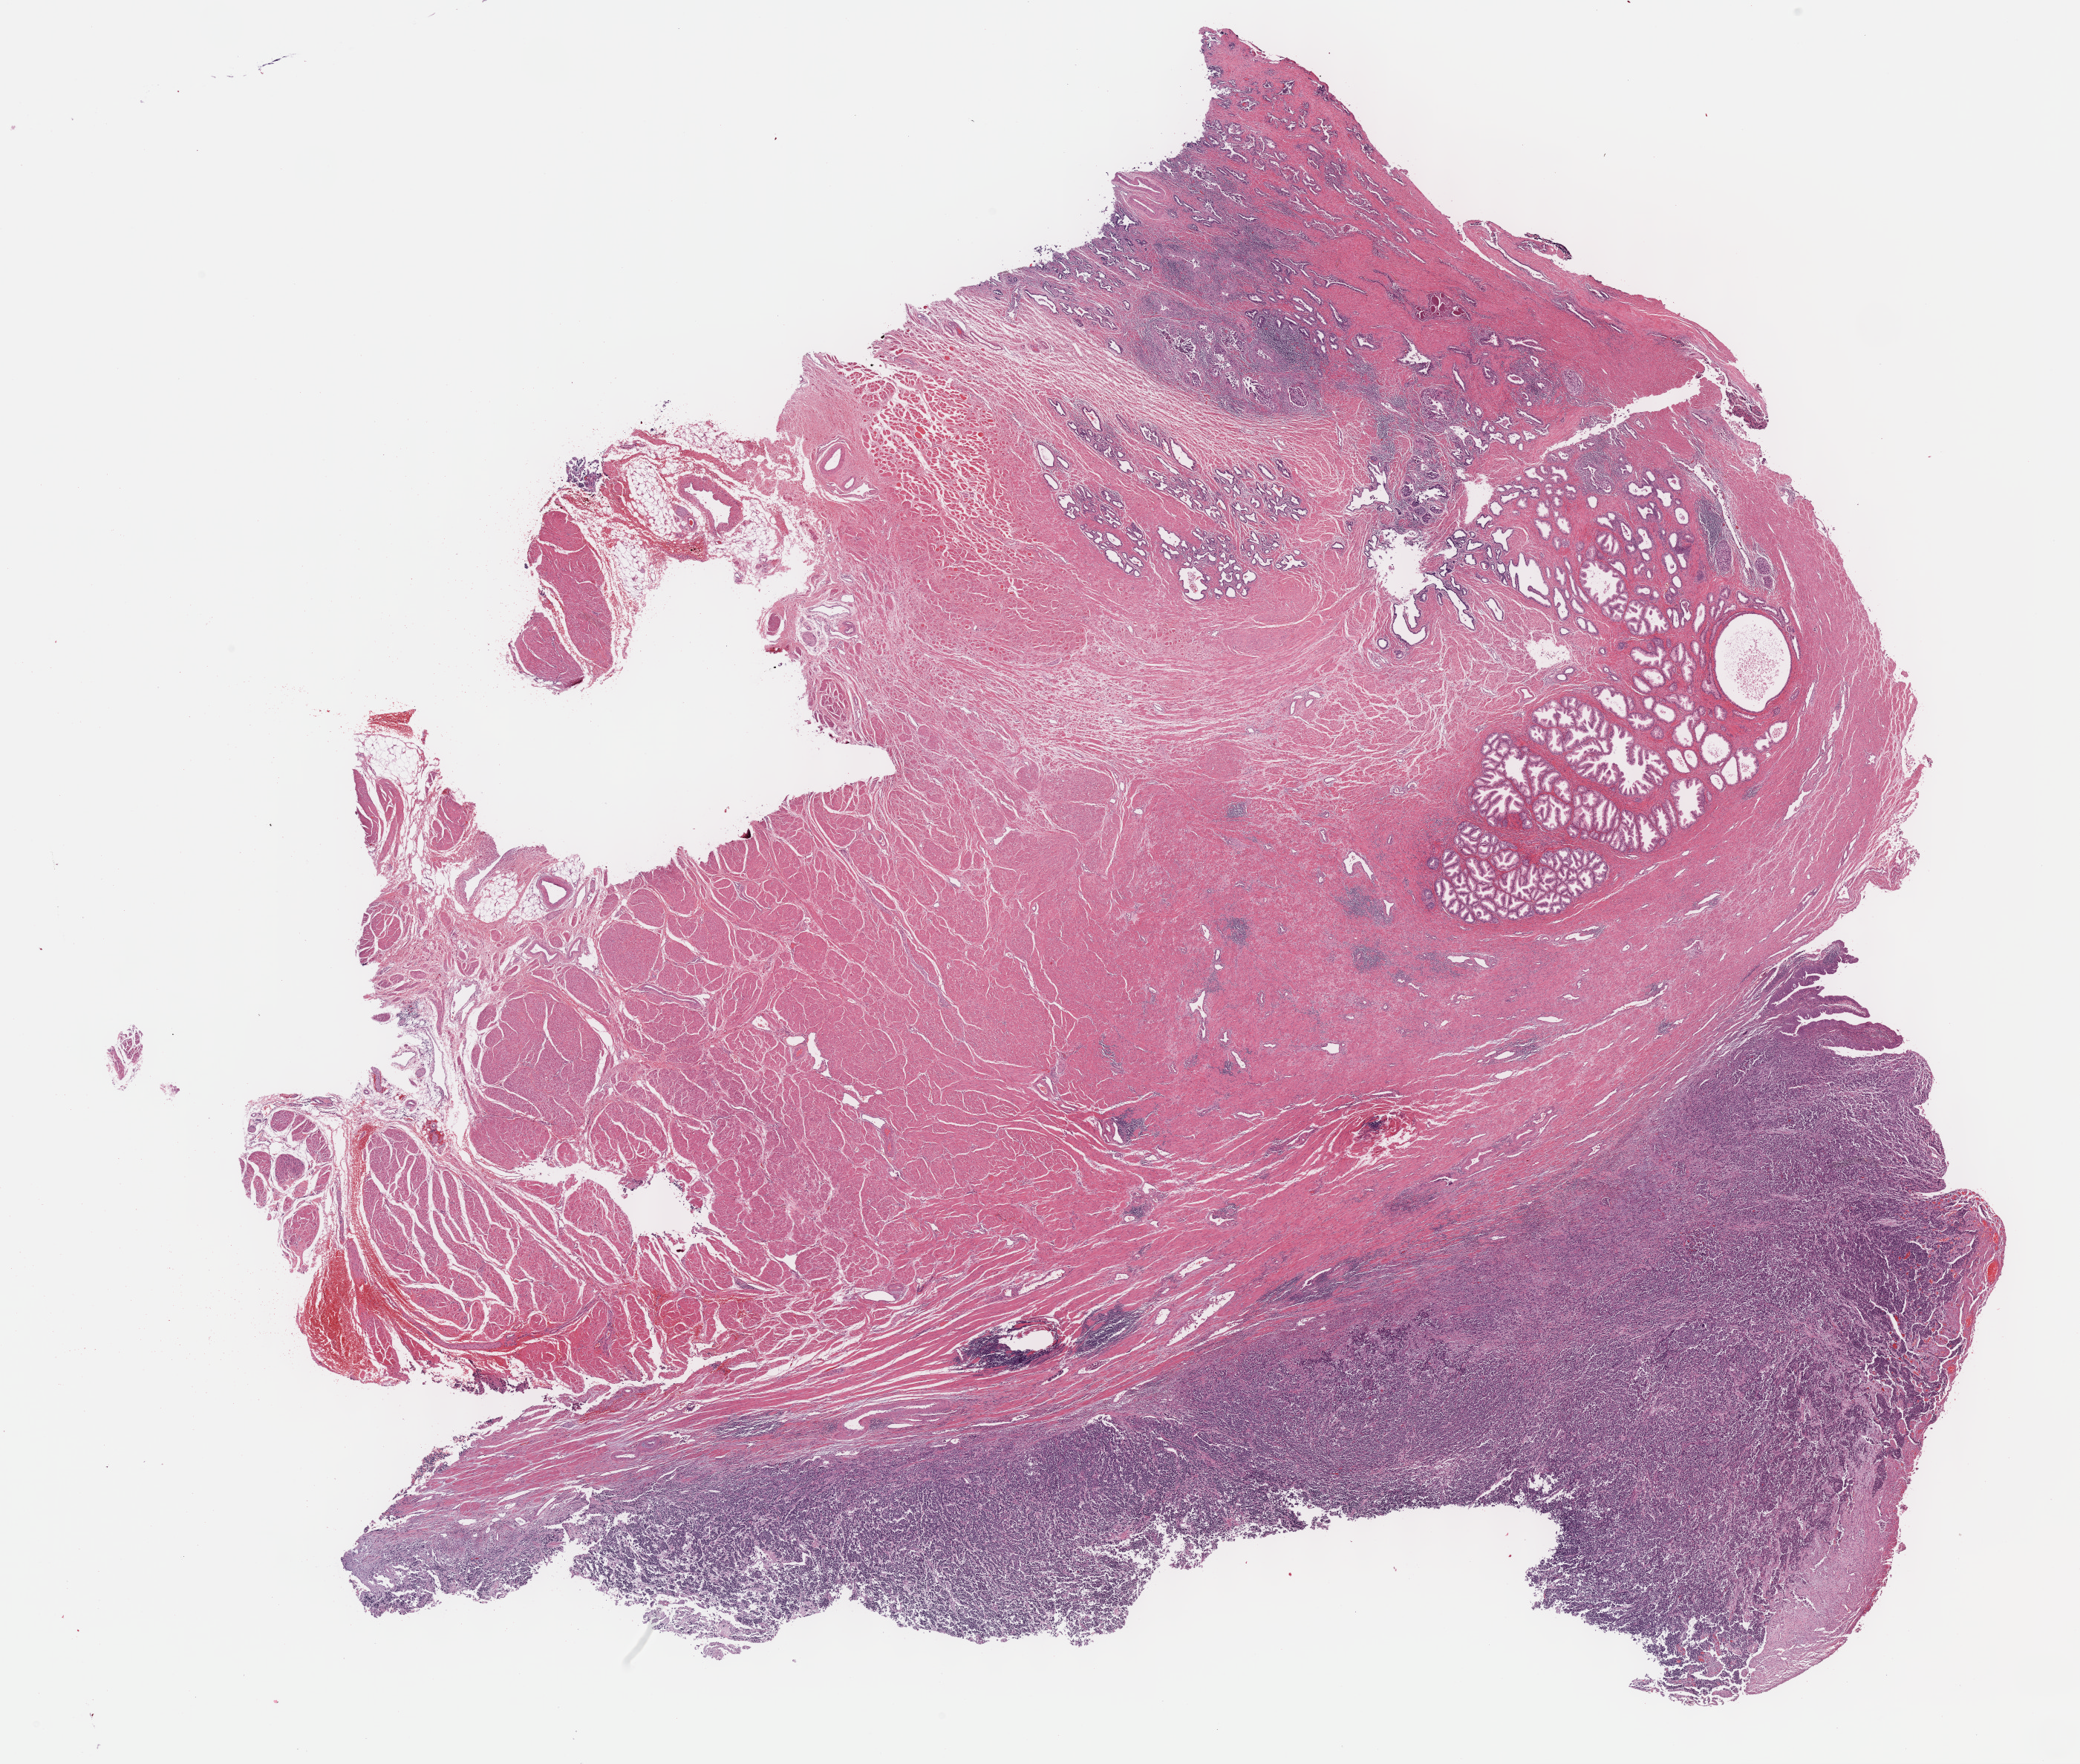
Digitized H&E tissue section (whole slide) — shown as a low-resolution overview of the whole scanned area (about 22.7 x 19.2 mm, acquisition: 40x scan), formalin-fixed paraffin-embedded (FFPE) diagnostic section, bladder, primary tumour sample. Male, age 49 years at initial diagnosis. Histologic grade: high grade.
- AJCC pathologic stage: III (6th edition)
- lymph nodes positive (case pathology): 0 of 51 examined
- histologic diagnosis: Transitional cell carcinoma